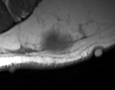
MRI of an extremity soft-tissue mass, one axial slice. Position 25 of 35 along the scan axis. MR volume resampled by the dataset authors to the PET/CT grid (not the native acquisition matrix). 115 × 90 image matrix, field of view 112 × 88 mm. Male patient. Case-level facts recorded for this patient, not image findings: histological type: pleiomorphic leiomyosarcoma; grade: high; site of the primary tumour: left buttock.
Structures marked on this image (expert contour drawn on MRI and transferred to this co-registered scan by the dataset authors):
- gross tumour volume including surrounding oedema: bounding box [x1, y1, x2, y2] px = [40, 28, 72, 58]
- gross tumour volume (mass): [40, 32, 68, 56]